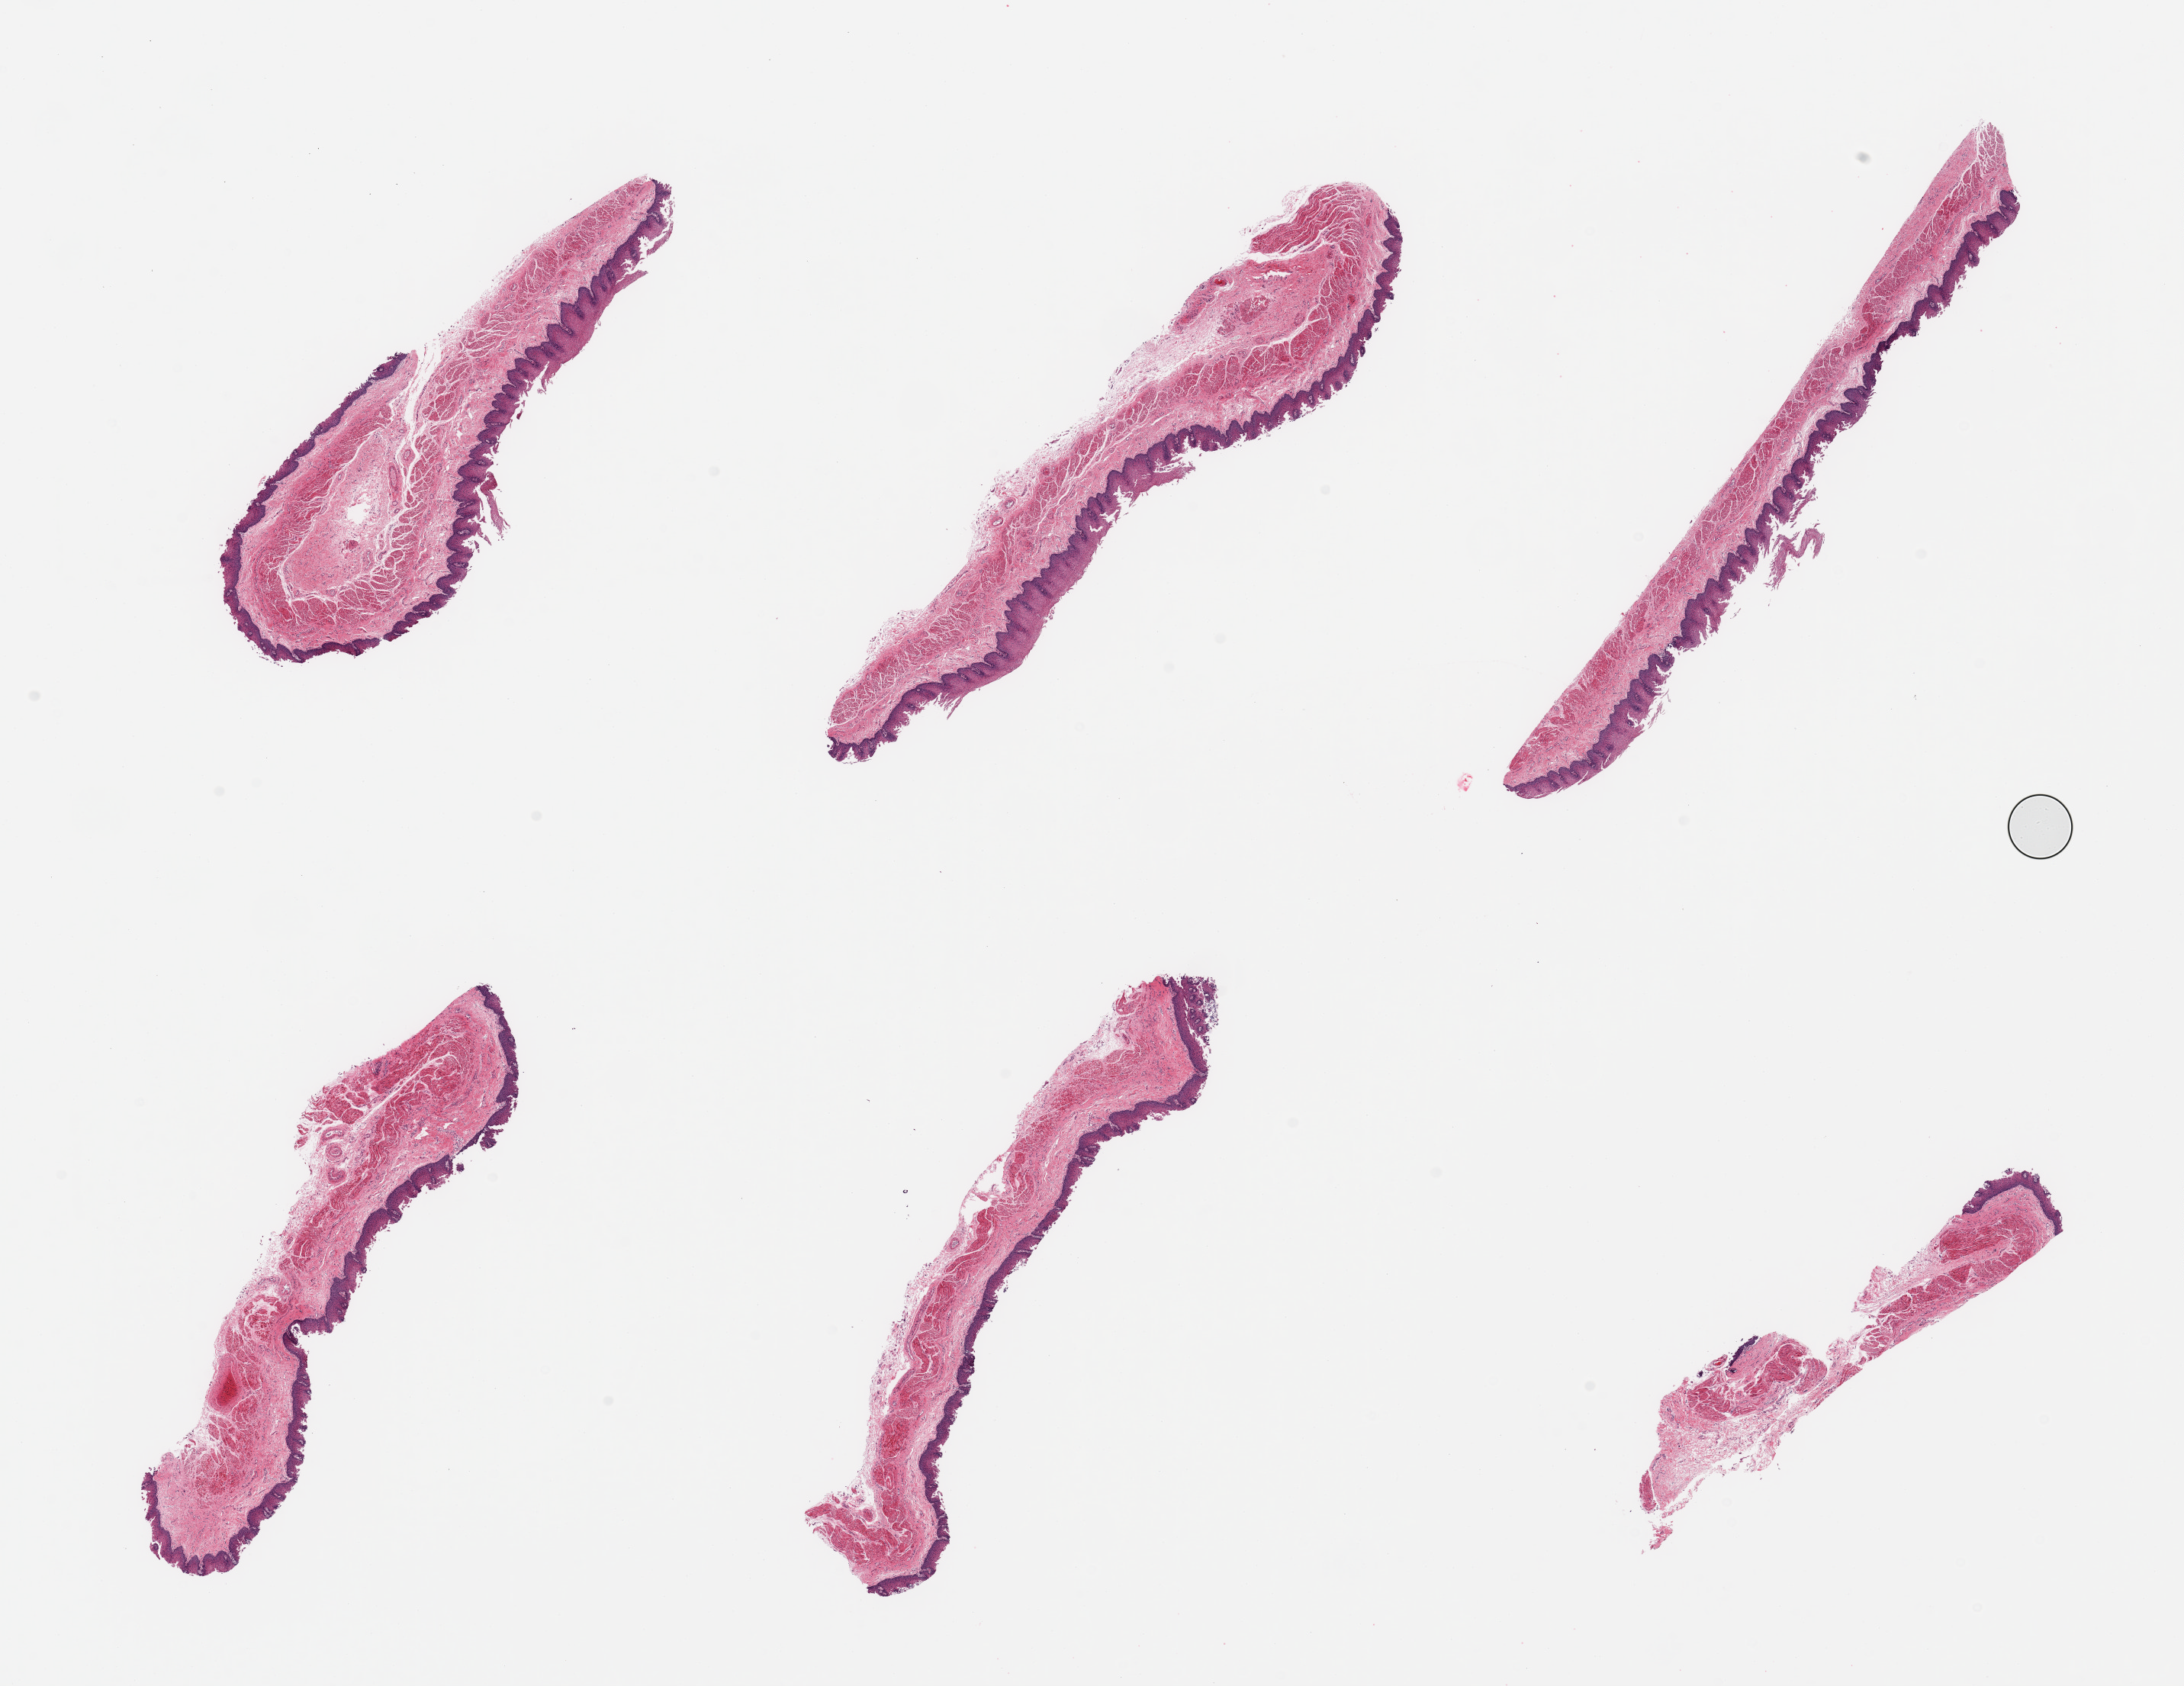
Whole-slide image, haematoxylin and eosin stain — whole scanned area (about 22.6 x 17.5 mm, acquisition: 20x scan) shown as a low-resolution overview; PAXgene-fixed paraffin-embedded (PFPE) section; sampled site (target tissue): esophageal mucous membrane; tissue donor sample. Male donor.
• review note (as recorded): 6 pieces, squamous mucosa is up to ~0.3mm, 100-25% thickness